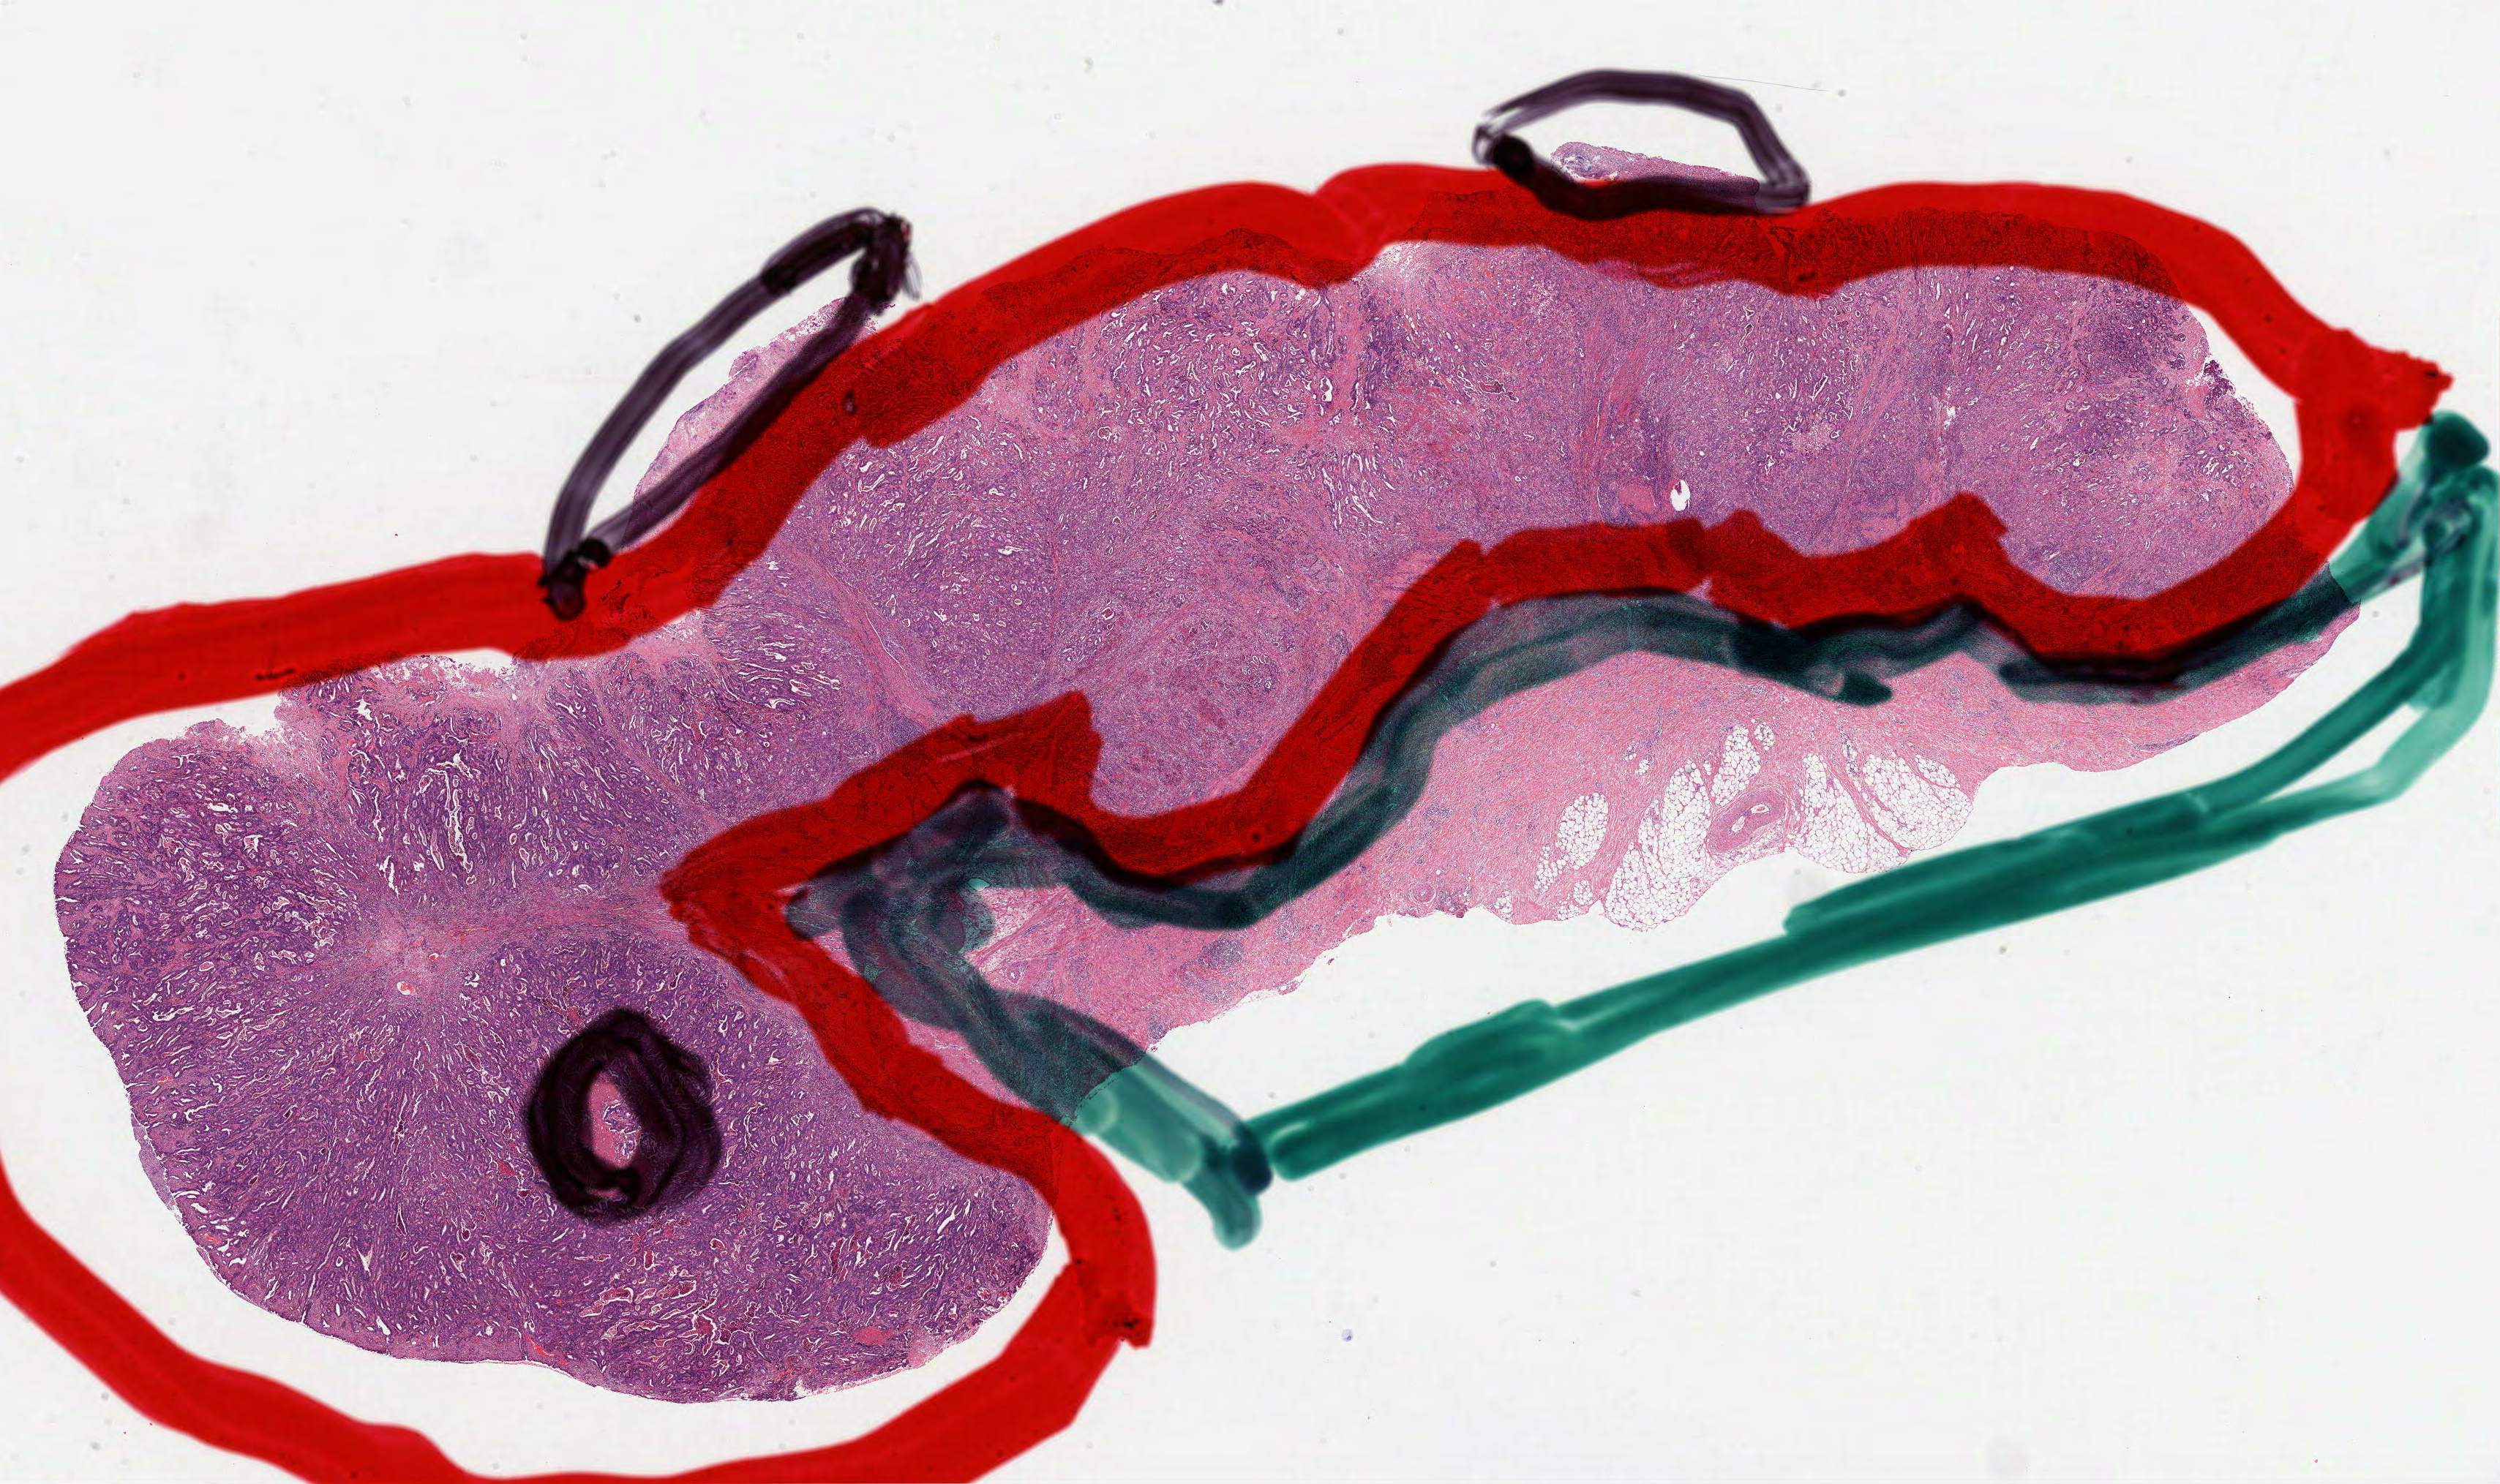
Whole-slide histology image, H&E — low-resolution overview of the scanned area, about 27.6 x 16.4 mm, formalin-fixed paraffin-embedded (FFPE) diagnostic section, sample: primary tumour, stomach. Male patient; age at initial diagnosis 74 years. Histologic grade: G3 (poorly differentiated).
Diagnosis: Adenocarcinoma, intestinal type (body of stomach). AJCC pathologic stage: IIB (7th edition).